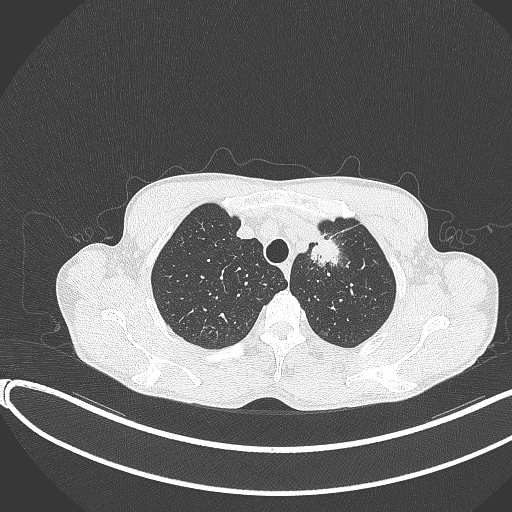
Chest CT, one axial slice; slice 322 of 374 in the series (ordered by position); reconstruction kernel B70f; lung window (W 1500 / L -600 HU); 1 mm slice thickness; 512 × 512 image matrix. Male patient, age 58 years. Case-level facts recorded for this patient, not image findings: clinical TNM (as recorded): T1c N1 M0.
Annotated regions visible in this slice (rectangle marked by the reading radiologist):
- lung tumour (recorded histology: adenocarcinoma): box from (x=298, y=219) to (x=343, y=277) px